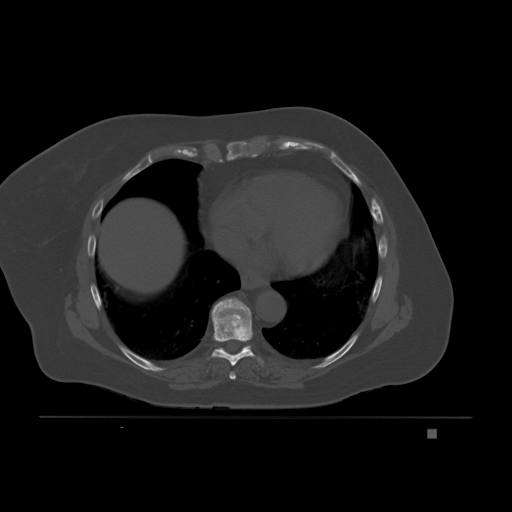
CT including the spine, one axial slice; position 117 of 221 along the scan axis; bone window (W 1800 / L 400 HU); 3 mm slice thickness; 512 × 512 image matrix. Patient: female, 63 years. From the clinical record (not read from this slice): primary cancer: breast.
Structures marked on this image (semi-automatic segmentation, software-assisted and operator-edited):
- T7 vertebra: bounding box [x1, y1, x2, y2] px = [229, 371, 236, 380]
- T8 vertebra: [211, 298, 264, 366]
- T9 vertebra: [213, 309, 251, 349]